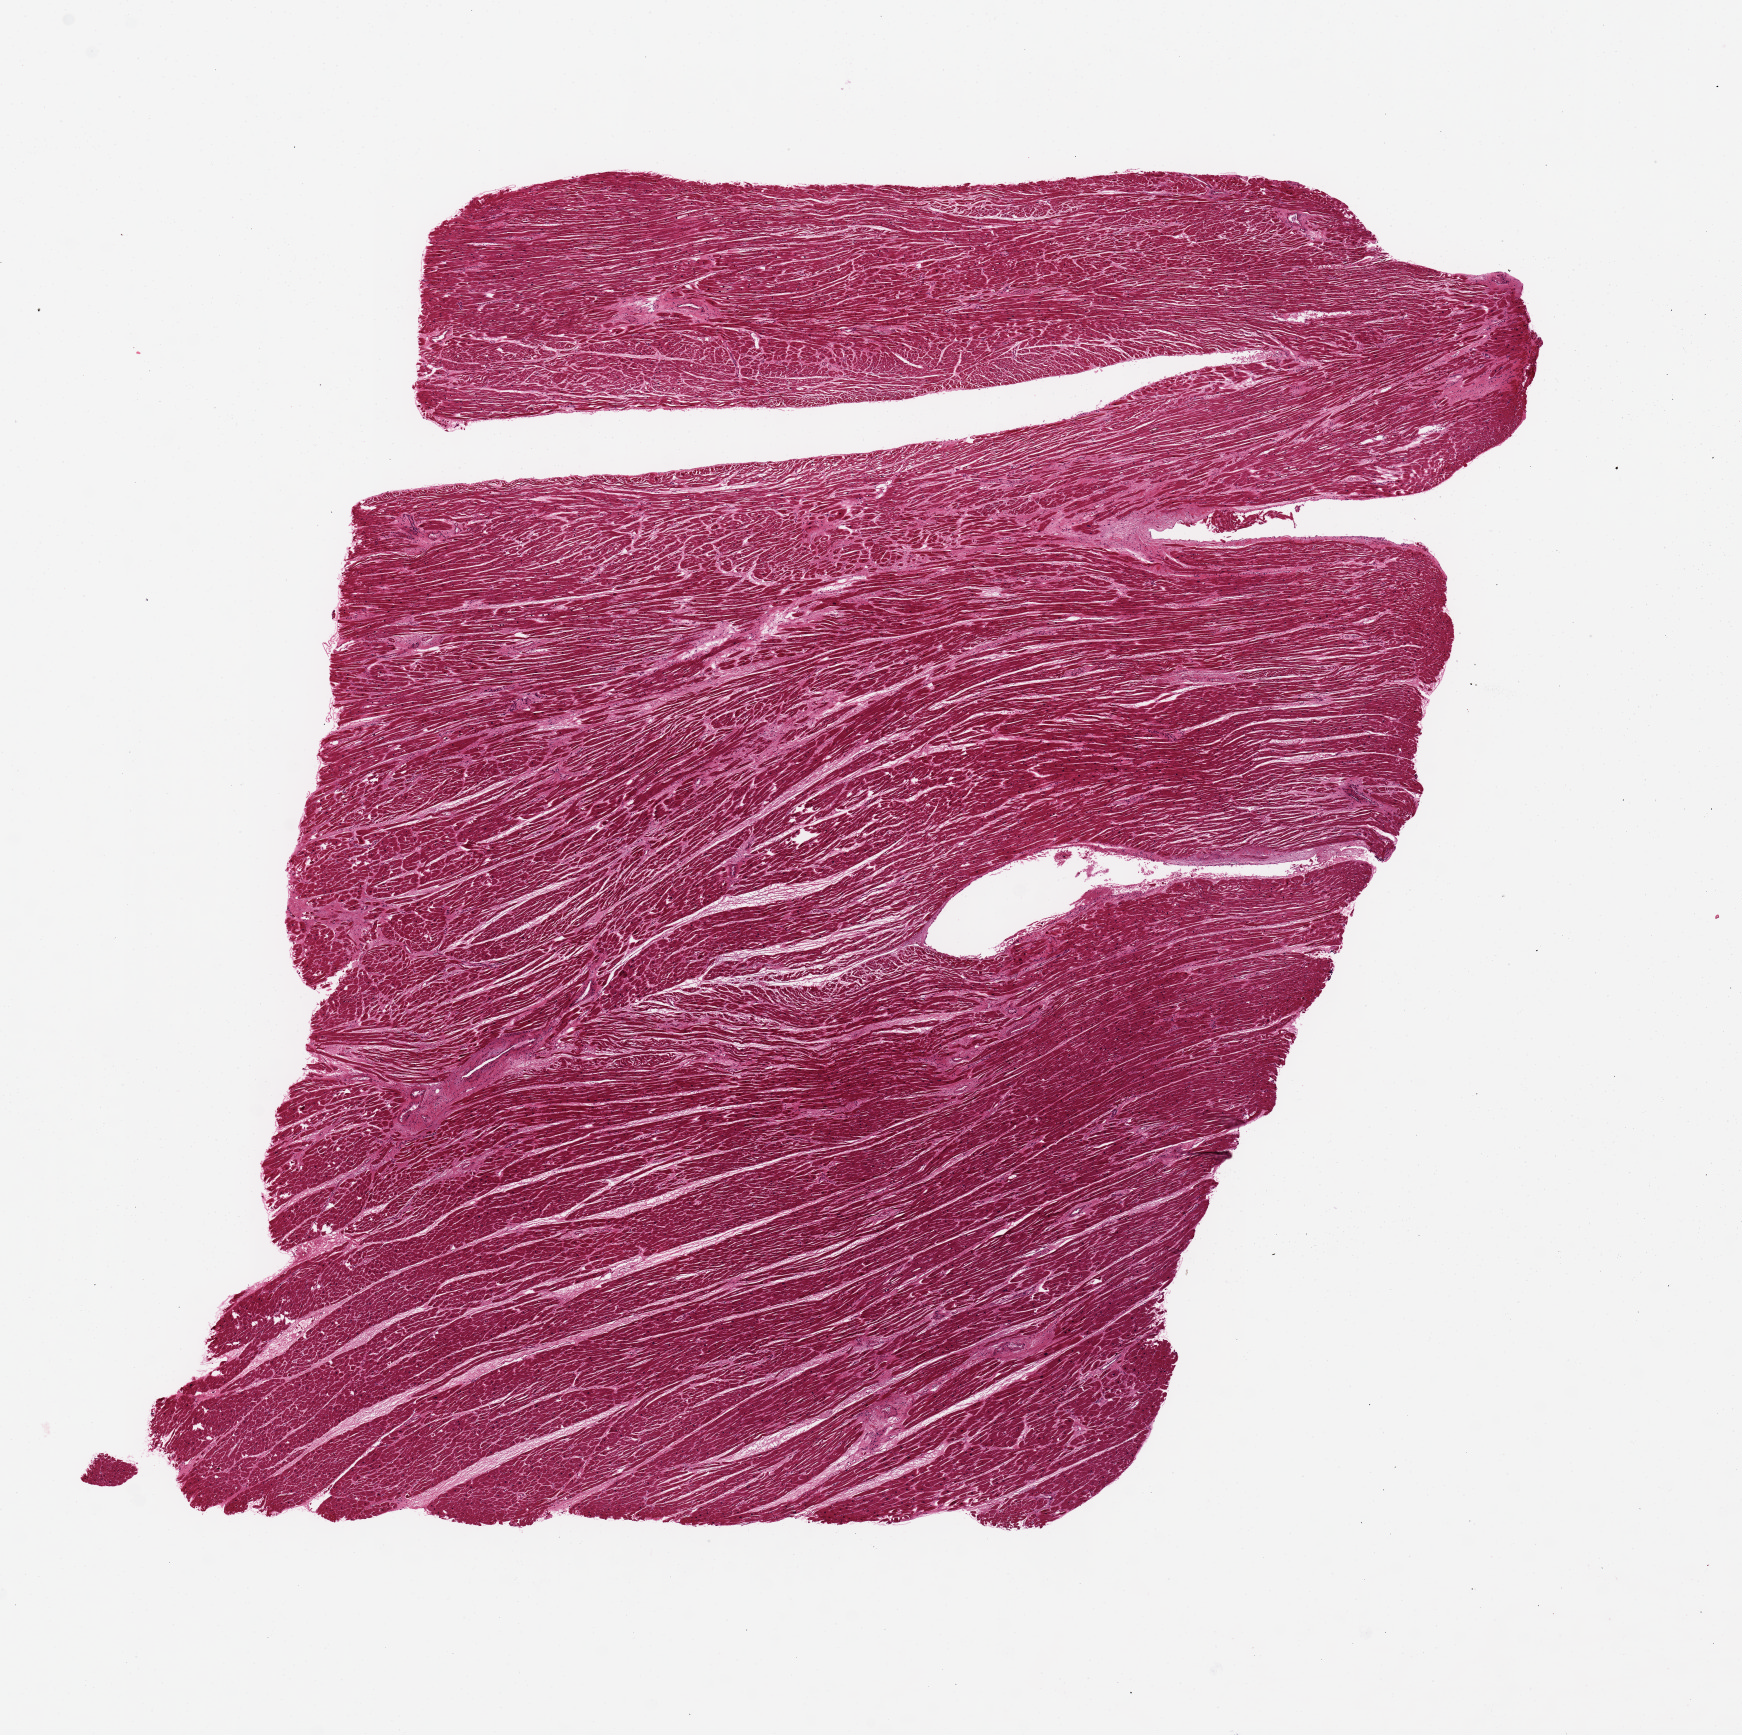
Haematoxylin and eosin whole-slide image — shown as a low-resolution overview of the whole scanned area (about 13.8 x 13.7 mm), PAXgene-fixed, paraffin-embedded tissue, sampled site (target tissue): heart, donor tissue sample. Donor sex: female.
Reviewer comment on this tissue sample: Mild interstitial fibrosis.